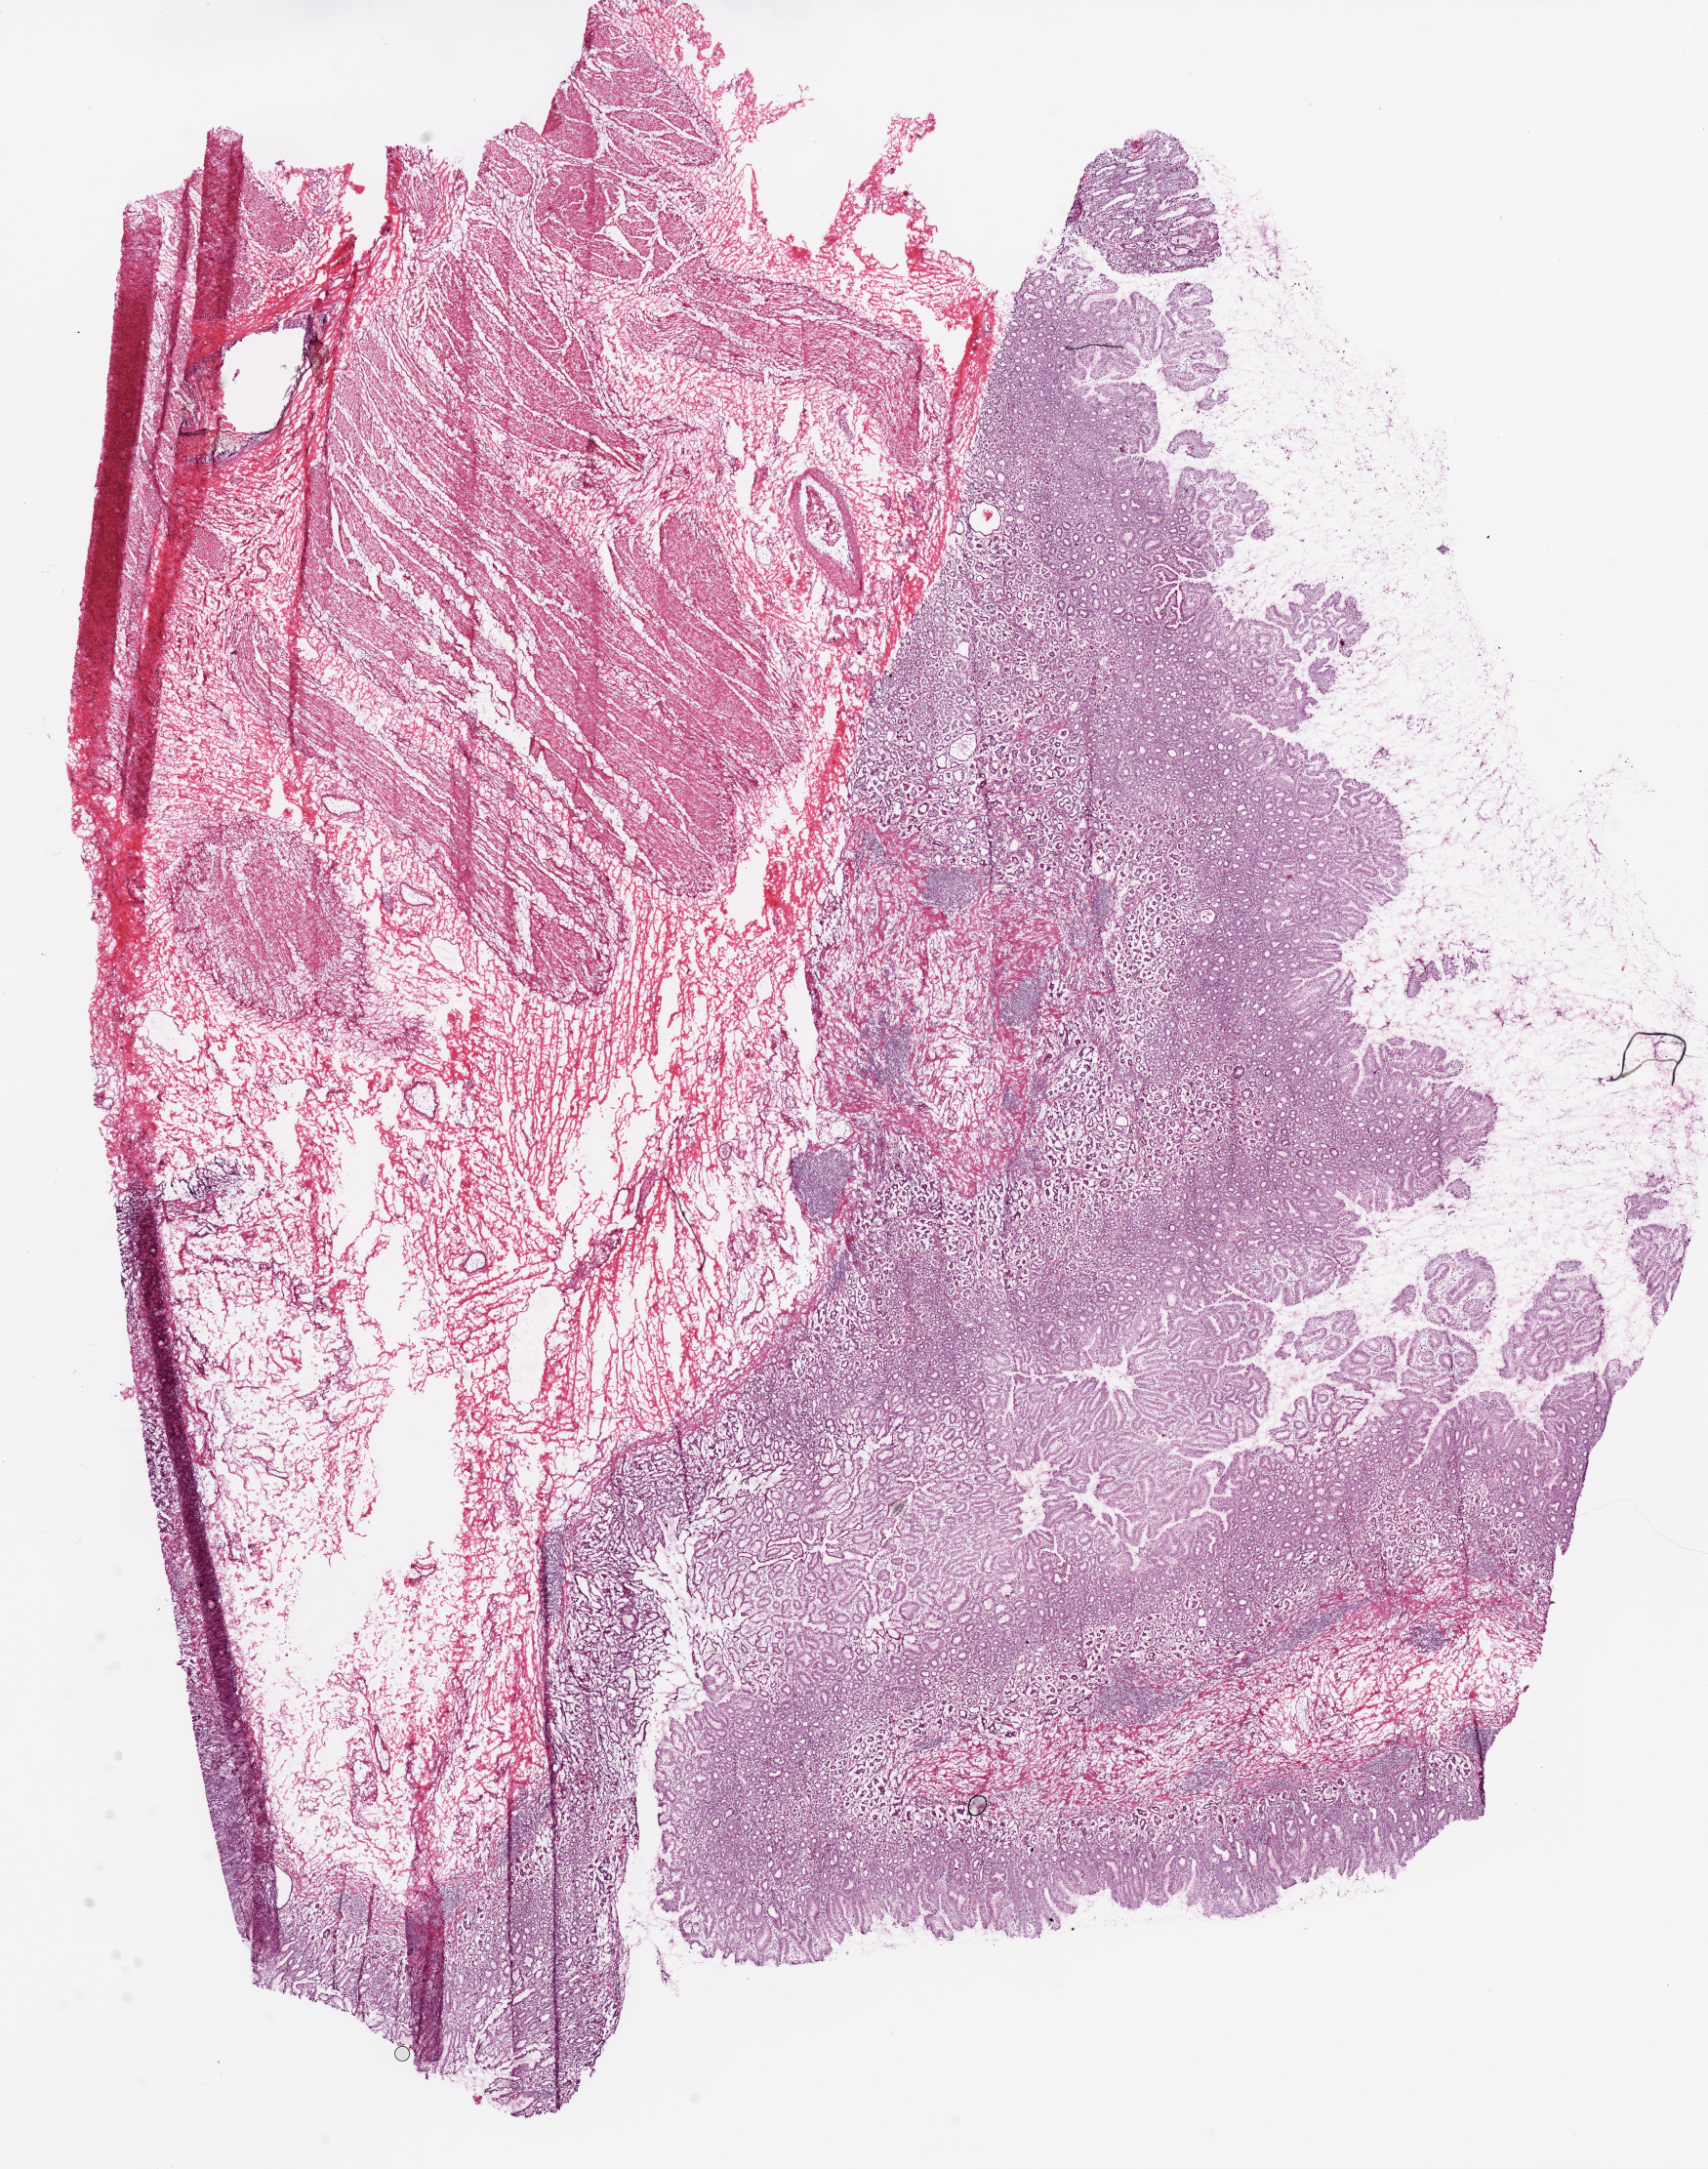
H&E-stained whole-slide image, shown as a low-resolution overview of the whole scanned area (about 14.0 x 17.8 mm, from a 20x scan); frozen section; sample: solid tissue normal (non-tumour tissue), stomach. Male patient; age at initial diagnosis 43 years.
This section: solid tissue normal (non-tumour) sample from the same patient. Patient diagnosis: Adenocarcinoma, NOS.